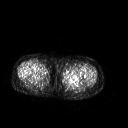
FDG PET of an extremity soft-tissue mass (from a PET/CT study), one axial slice. Position 226 of 267 along the scan axis. 3.27 mm slice thickness. 128 × 128 image matrix, field of view 500 × 500 mm. Patient: female, 42 years. From the clinical record (not read from this slice): histological type: pleiomorphic leiomyosarcoma; grade: intermediate; site of the primary tumour: left thigh.
Annotated regions visible in this slice (expert contour drawn on MRI and transferred to this co-registered scan by the dataset authors):
- gross tumour volume including surrounding oedema: bounding box [x1, y1, x2, y2] px = [63, 69, 81, 81]